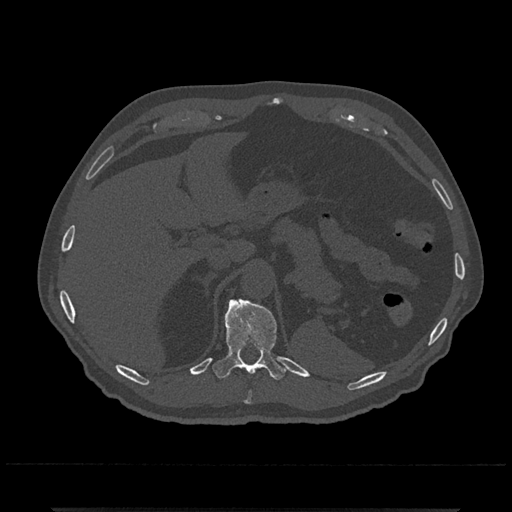
CT including the spine, one axial slice; slice 501 of 797 in the series (ordered by position); bone window (W 1800 / L 400 HU); 512 × 512 image matrix, field of view 393 × 393 mm. Male patient, age 67 years. From the clinical record (not read from this slice): primary cancer: prostate.
Structures marked on this image (semi-automatic segmentation, software-assisted and operator-edited):
- T10 vertebra: bounding box [x1, y1, x2, y2] px = [245, 391, 252, 404]
- T11 vertebra: [212, 298, 286, 380]